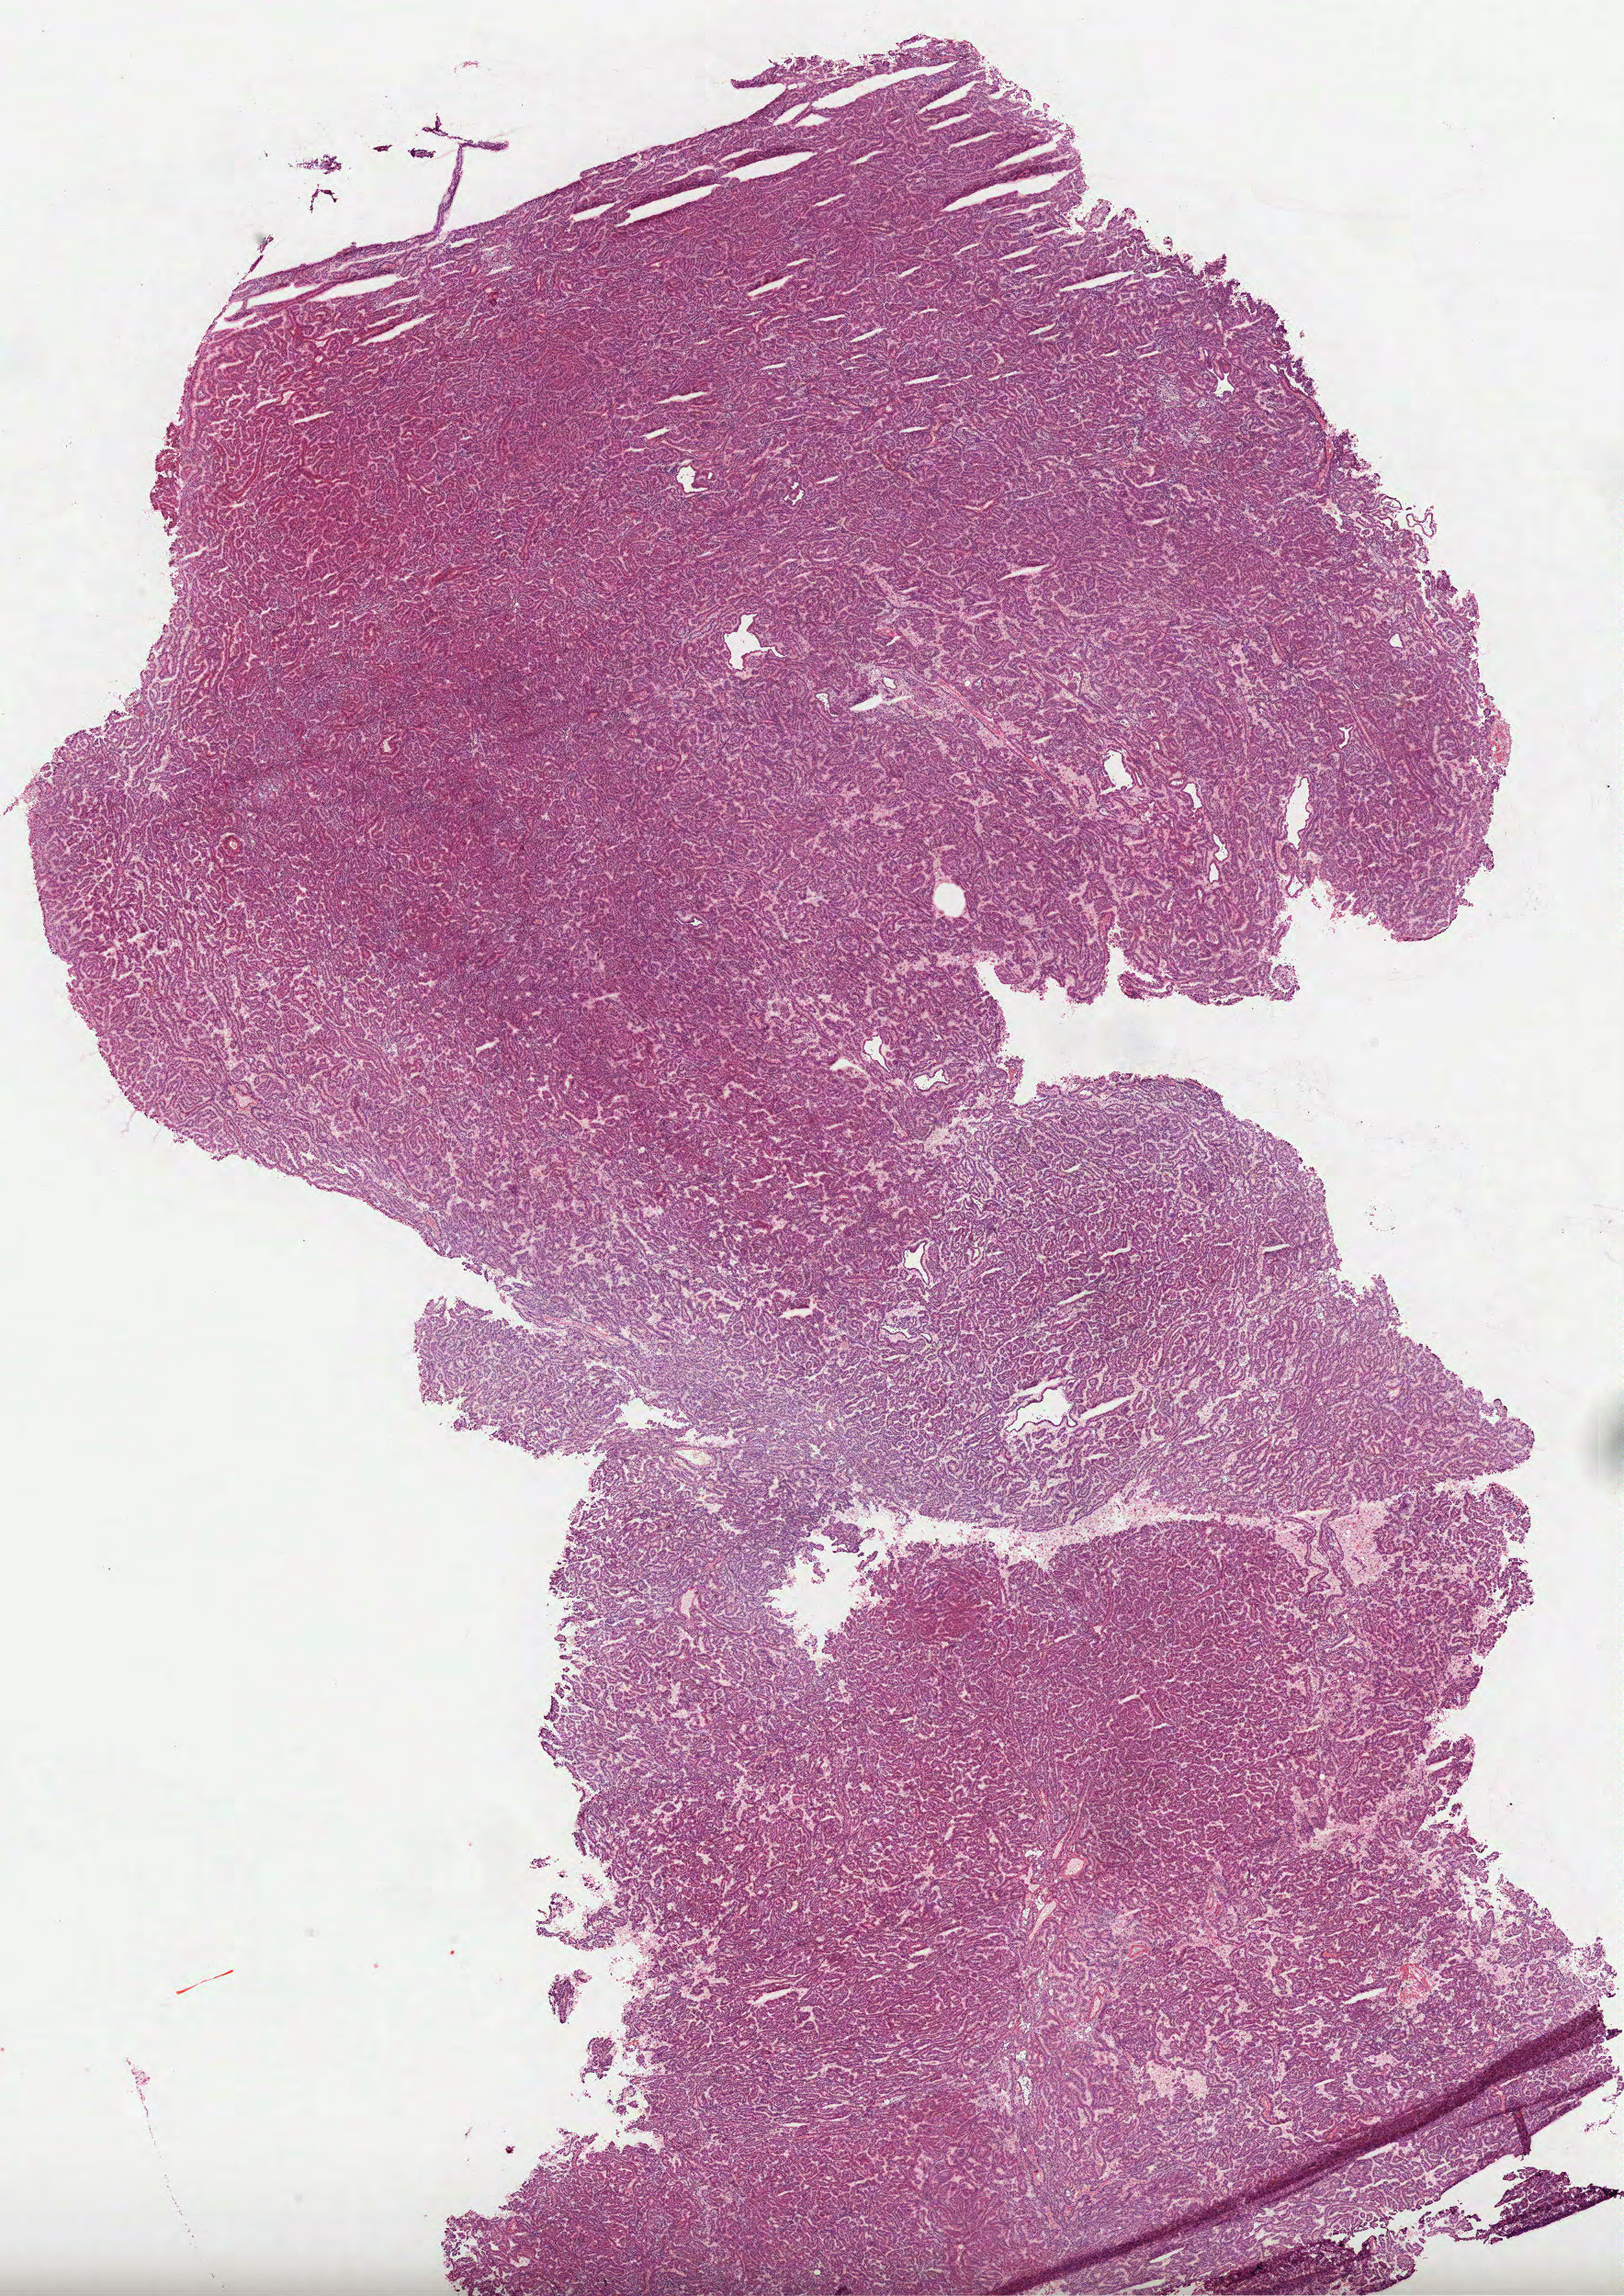
Digitized H&E tissue section (whole slide) — whole scanned area (about 14.3 x 20.2 mm) shown as a low-resolution overview, frozen section from the top of the tissue portion, sample: primary tumour, kidney. Male patient; age at initial diagnosis 74 years. Composition of this section per pathologist review: tumour cells 100%, tumour nuclei 90%, normal cells 0%, stromal cells 0%, necrosis 0%. Inflammatory infiltration, as recorded: lymphocyte infiltration 1%, monocyte infiltration 1%, neutrophil infiltration 0%.
Lymph nodes positive (case pathology): 0 of 5 examined. AJCC pathologic stage: II (6th edition). Histologic diagnosis: Papillary adenocarcinoma, NOS.